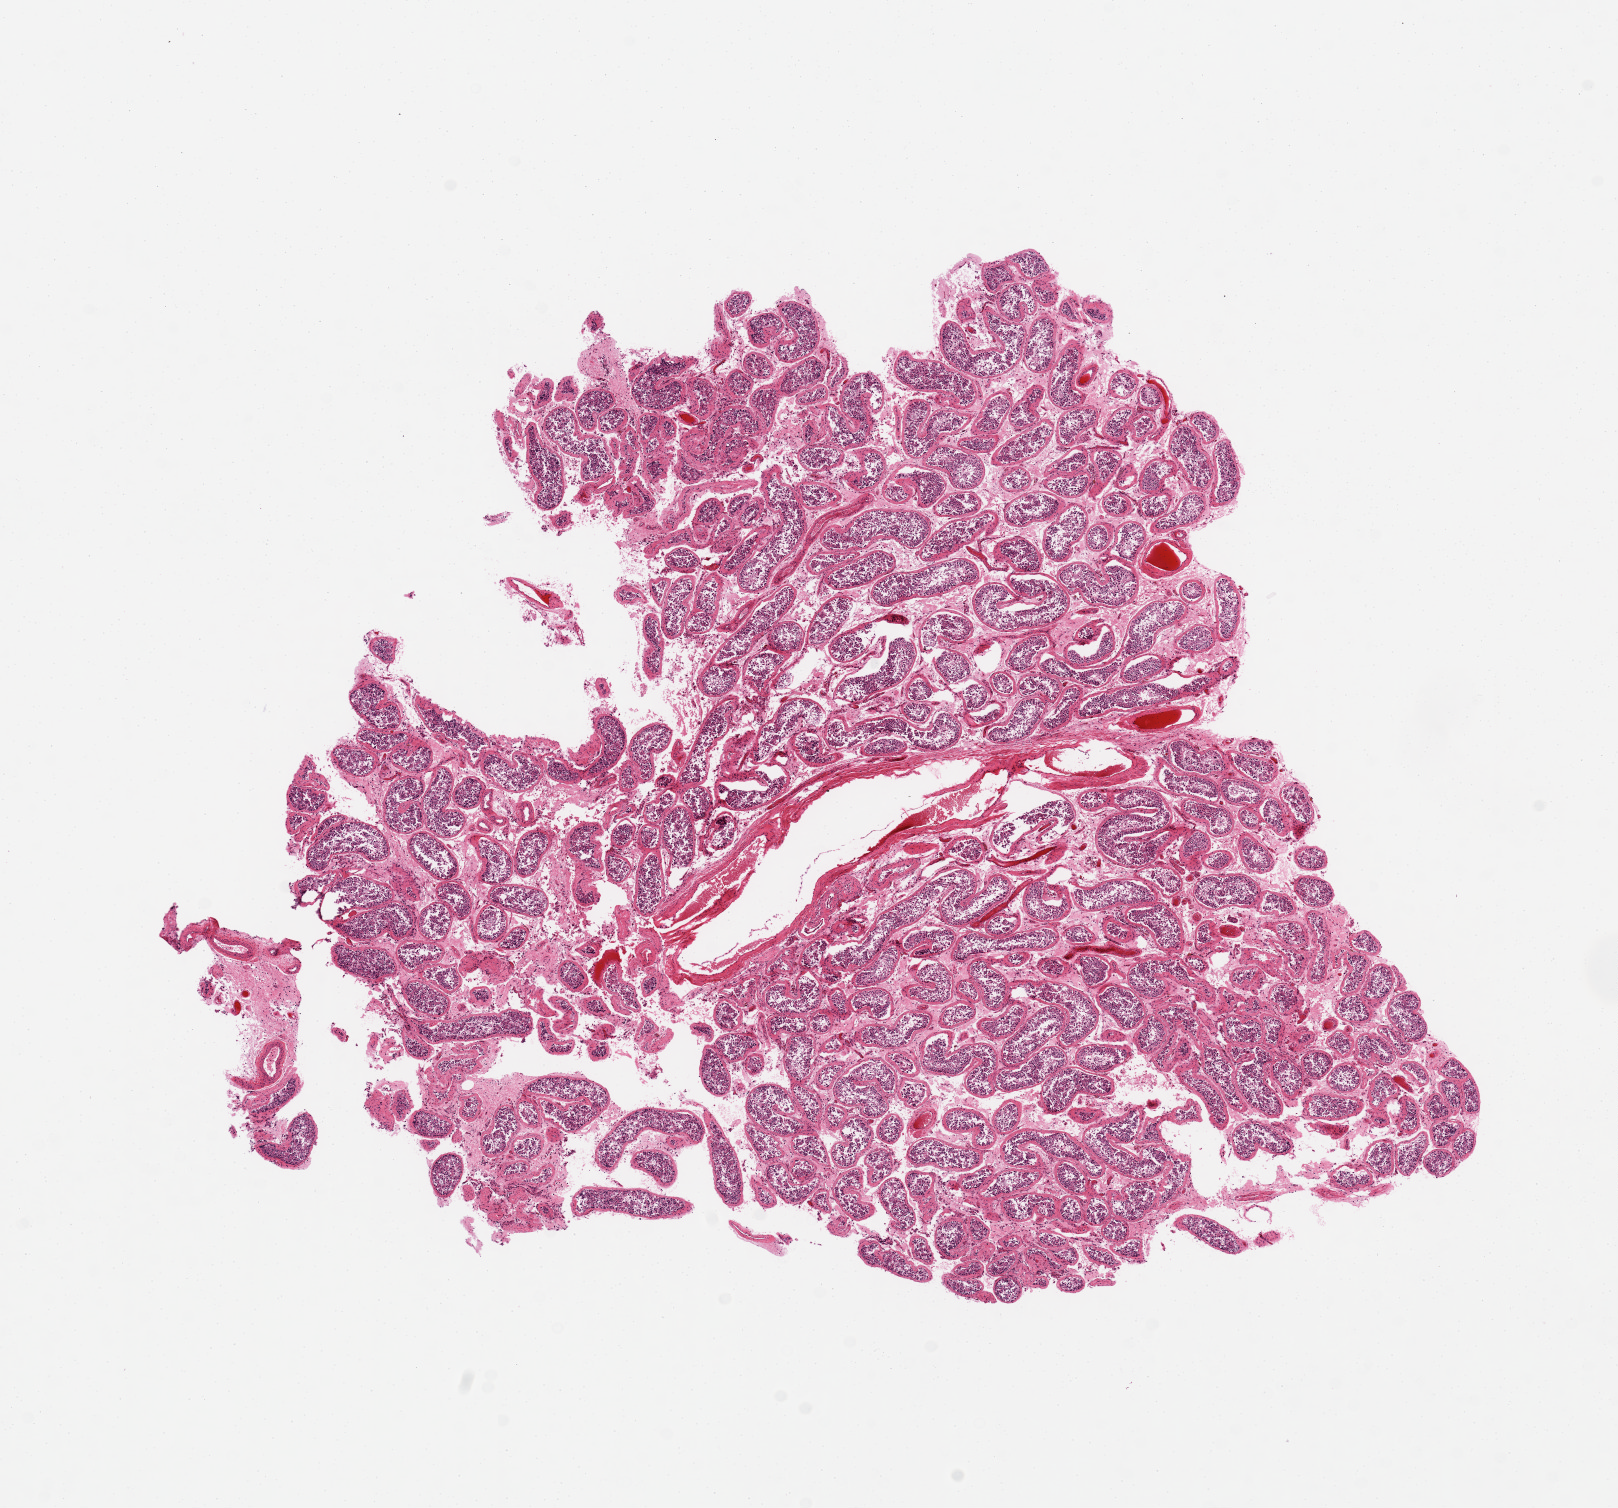
Hematoxylin and eosin (H&E) whole-slide image, whole scanned area (about 12.8 x 11.9 mm) shown as a low-resolution overview, PAXgene-fixed, paraffin-embedded tissue, target tissue: testis, tissue donor sample. Donor sex: male.
Reviewer comment on this tissue sample: Reduced spermatogenesis. 8.2x8.